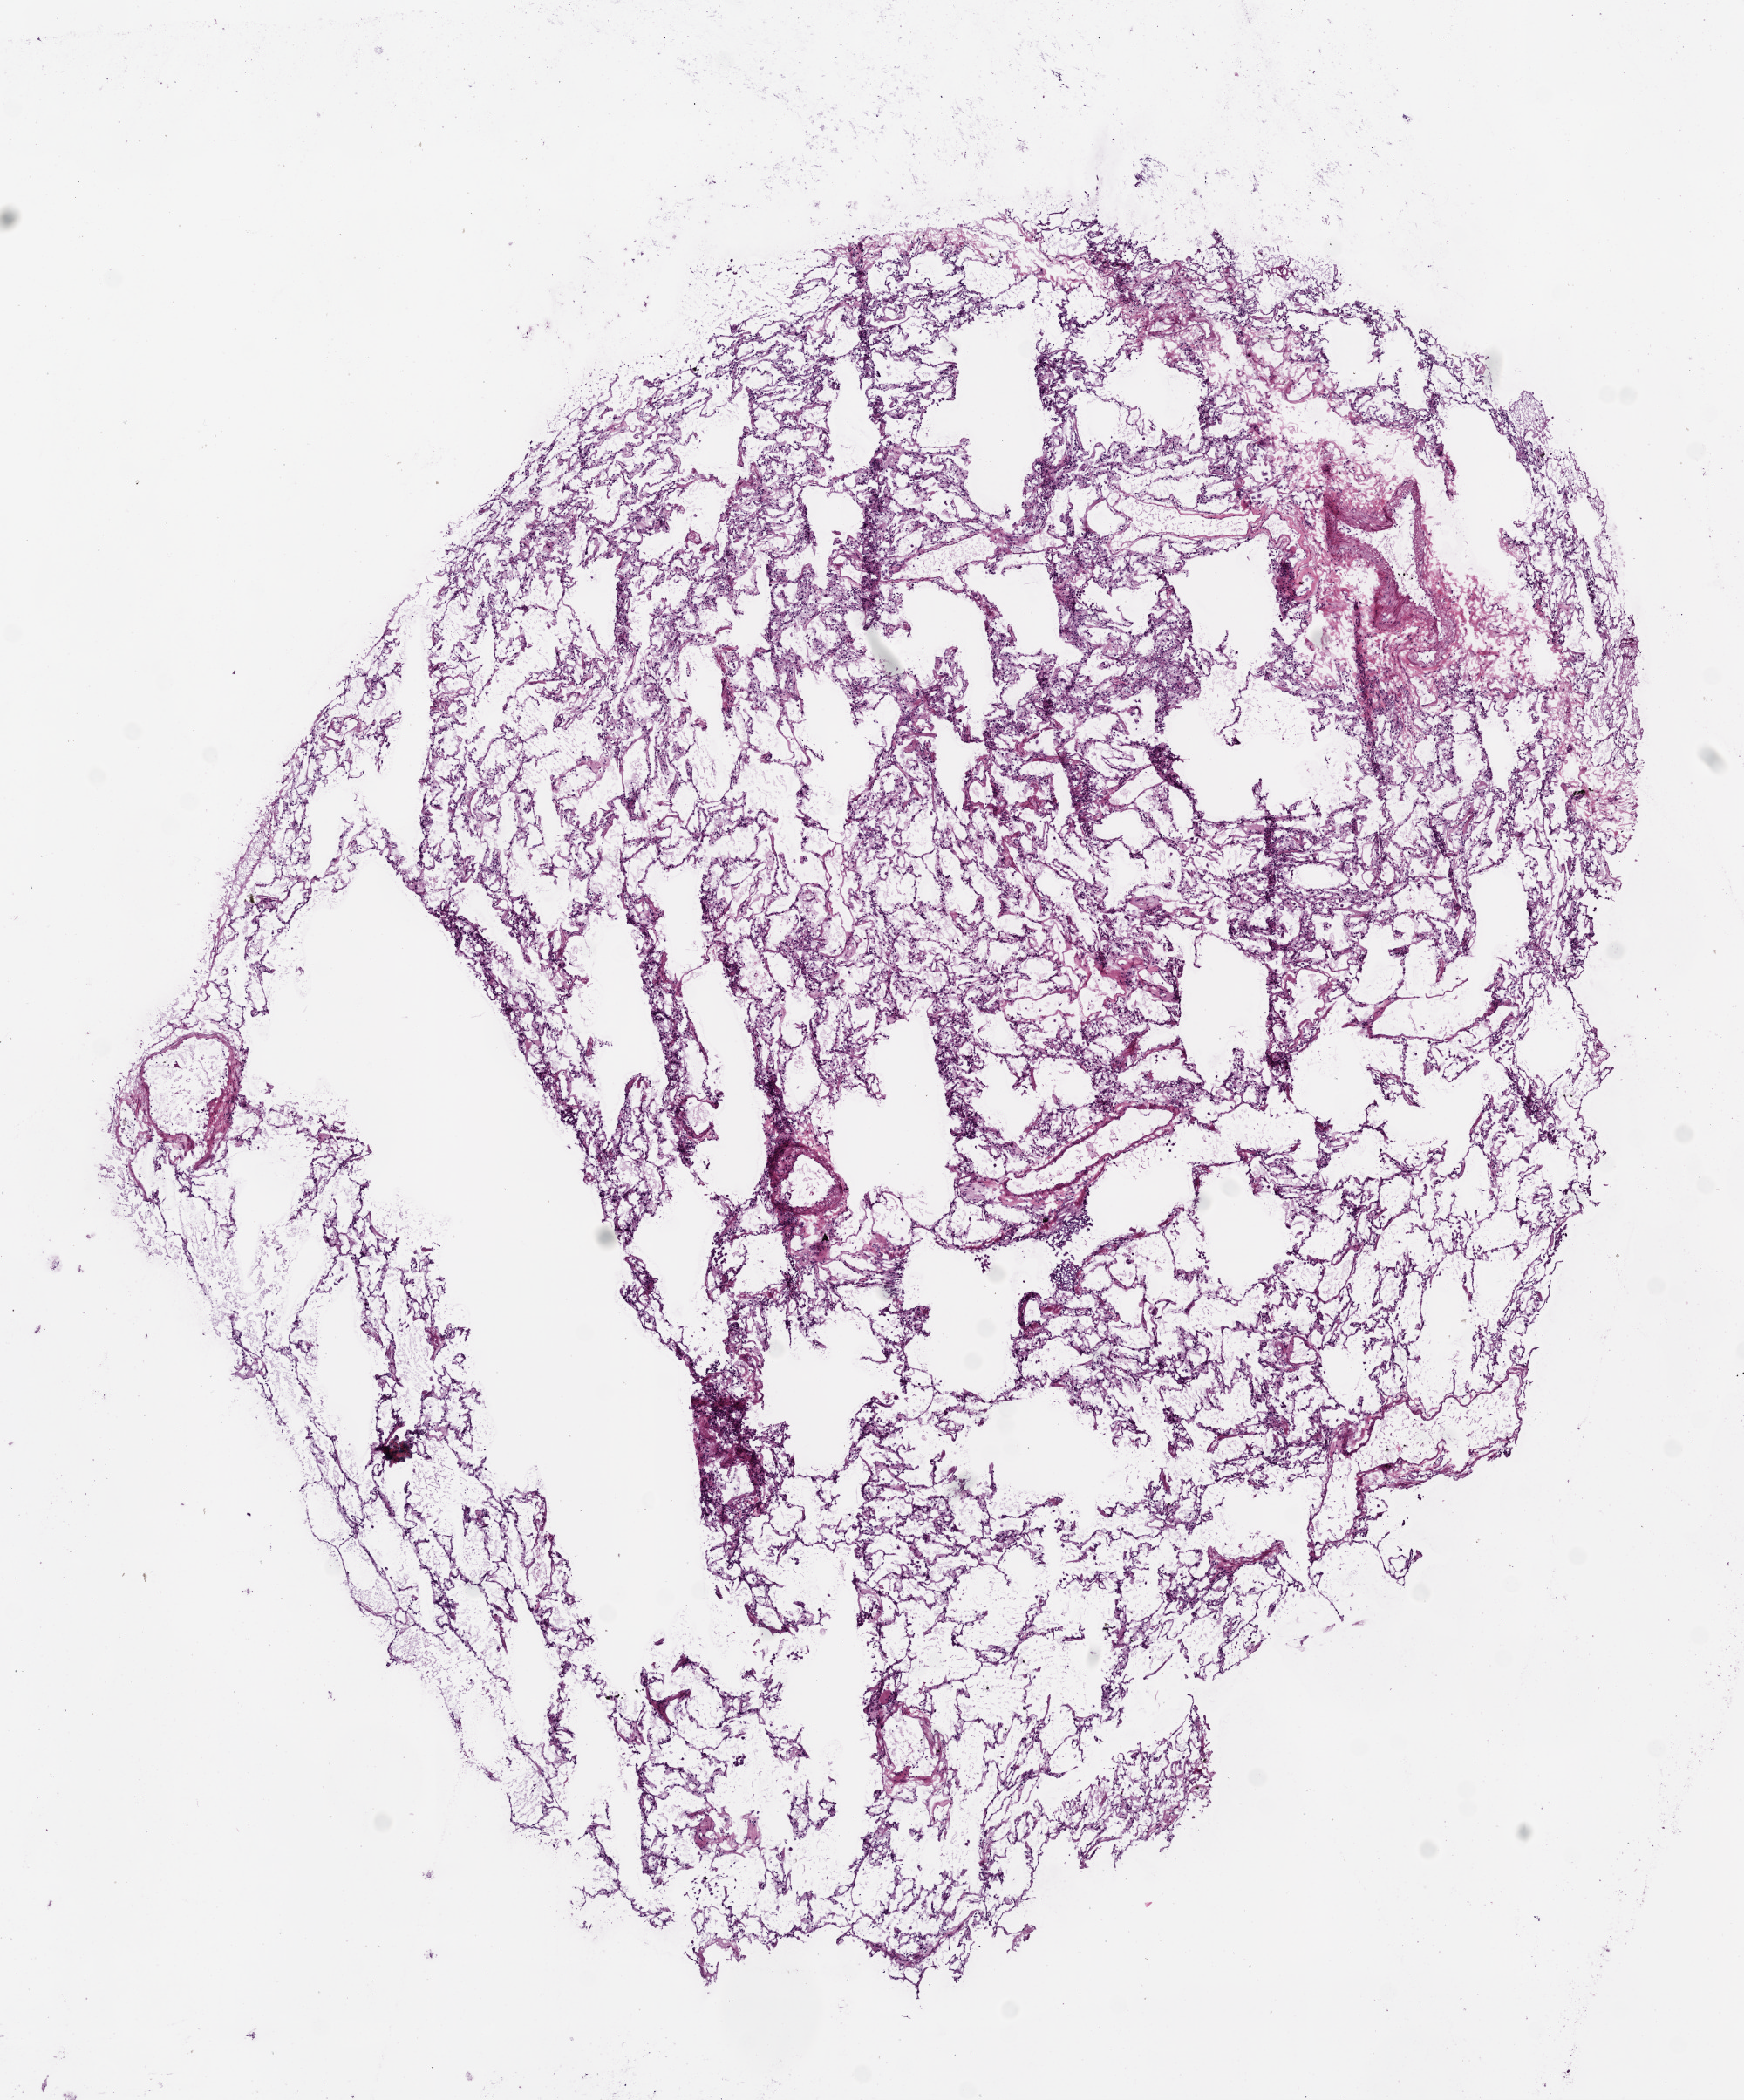
Whole-slide histology image, H&E — a low-resolution overview of the entire scanned area, about 8.0 x 9.7 mm (from a 20x scan), frozen section from the bottom of the tissue portion, solid tissue normal (non-tumour tissue) sample from the lung. Female patient; age at initial diagnosis 67 years.
This section: solid tissue normal (non-tumour) sample from the same patient. Patient diagnosis: Adenocarcinoma, NOS (upper lobe, lung).